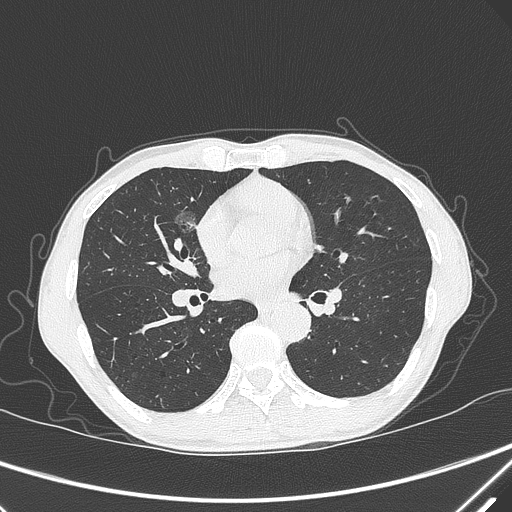
Chest CT, one axial slice. Lung window (W 1500 / L -600 HU). 1 mm slice thickness. 512 × 512 image matrix, field of view 350 × 350 mm. Male patient, age 67 years. From the clinical record (not read from this slice): clinical TNM (as recorded): T1c N0 M0; histopathological grade: G1-2.
Annotated regions visible in this slice (bounding box drawn by a radiologist):
- lung tumour (recorded histology: adenocarcinoma): bounding box (x1, y1, x2, y2) in pixels: (163, 200, 206, 242)